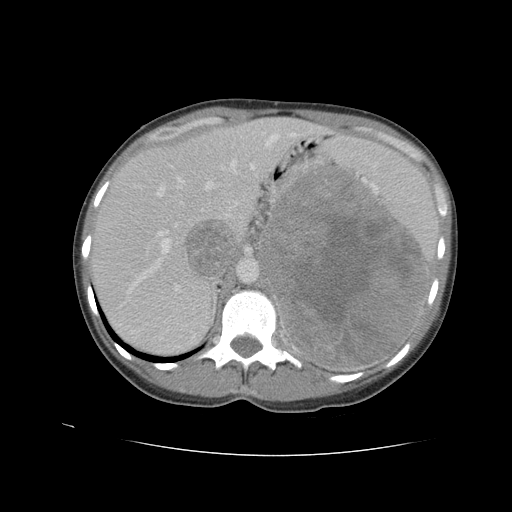
Contrast-enhanced abdominal CT, one axial slice. Slice 71 of 90 in the series (ordered by position). 120 kVp. Intravenous contrast given. Soft-tissue window (W 400 / L 40 HU). 512 × 512 image matrix, field of view 360 × 360 mm. Female patient. Case-level facts recorded for this patient, not image findings: diagnosis: adrenocortical carcinoma; tumour side: left adrenal; tumour size at pathology: 18 cm; Ki-67 index: 11 %; stage (as recorded): 3.
Structures marked on this image (semi-automatic segmentation, software-assisted and operator-edited):
- mass: bounding box [x1, y1, x2, y2] px = [261, 165, 428, 370]